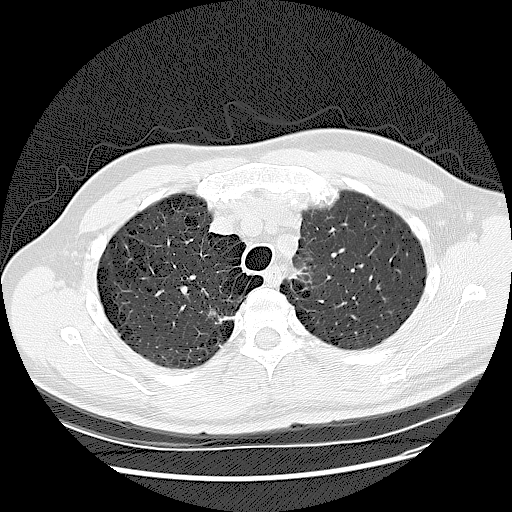
Low-dose screening chest CT, one axial slice. Slice 104 of 132 in the series (ordered by position). Reconstruction kernel LUNG. Lung window (W 1500 / L -600 HU). 2.5 mm slice thickness. 512 × 512 image matrix, field of view 380 × 380 mm.
Annotated regions visible in this slice (expert manual segmentation):
- lesion 1 (tumor, upper lobe of right lung): bounding box [x1, y1, x2, y2] px = [207, 308, 228, 324]